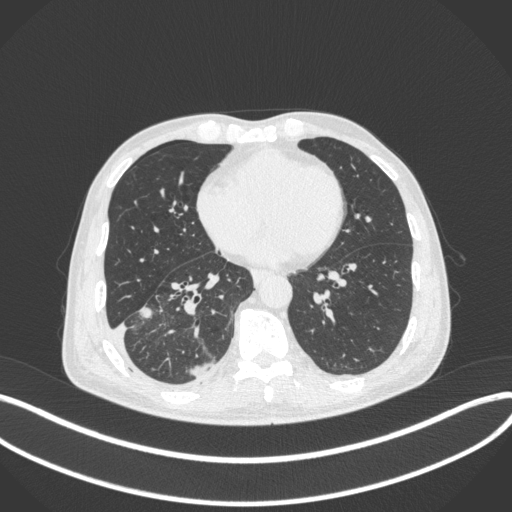
Chest CT, one axial slice; slice 149 of 385 in the series (ordered by position); reconstruction kernel B31f; 120 kVp; lung window (W 1500 / L -600 HU); 1 mm slice thickness; 512 × 512 image matrix, field of view 400 × 400 mm. Patient: male, 64 years. Case-level facts recorded for this patient, not image findings: clinical TNM (as recorded): T3 N0 M0; histopathological grade: G2-3.
Outlined on this slice (rectangle marked by the reading radiologist):
- lung tumour (recorded histology: adenocarcinoma): bounding box <140,300,154,320> (left, top, right, bottom; pixels)